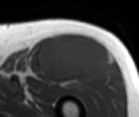
MRI of an extremity soft-tissue mass, one axial slice. Slice 65 of 86 in the series (ordered by position). MR volume resampled by the dataset authors to the PET/CT grid (not the native acquisition matrix). 3.27 mm slice thickness. 139 × 117 image matrix. Male patient. Case-level facts recorded for this patient, not image findings: histological type: extraskeletal osteosarcoma; grade: high; site of the primary tumour: thigh.
Annotated regions visible in this slice (expert contour drawn on MRI and transferred to this co-registered scan by the dataset authors):
- gross tumour volume (mass): bounding box <38,34,110,81> (left, top, right, bottom; pixels)